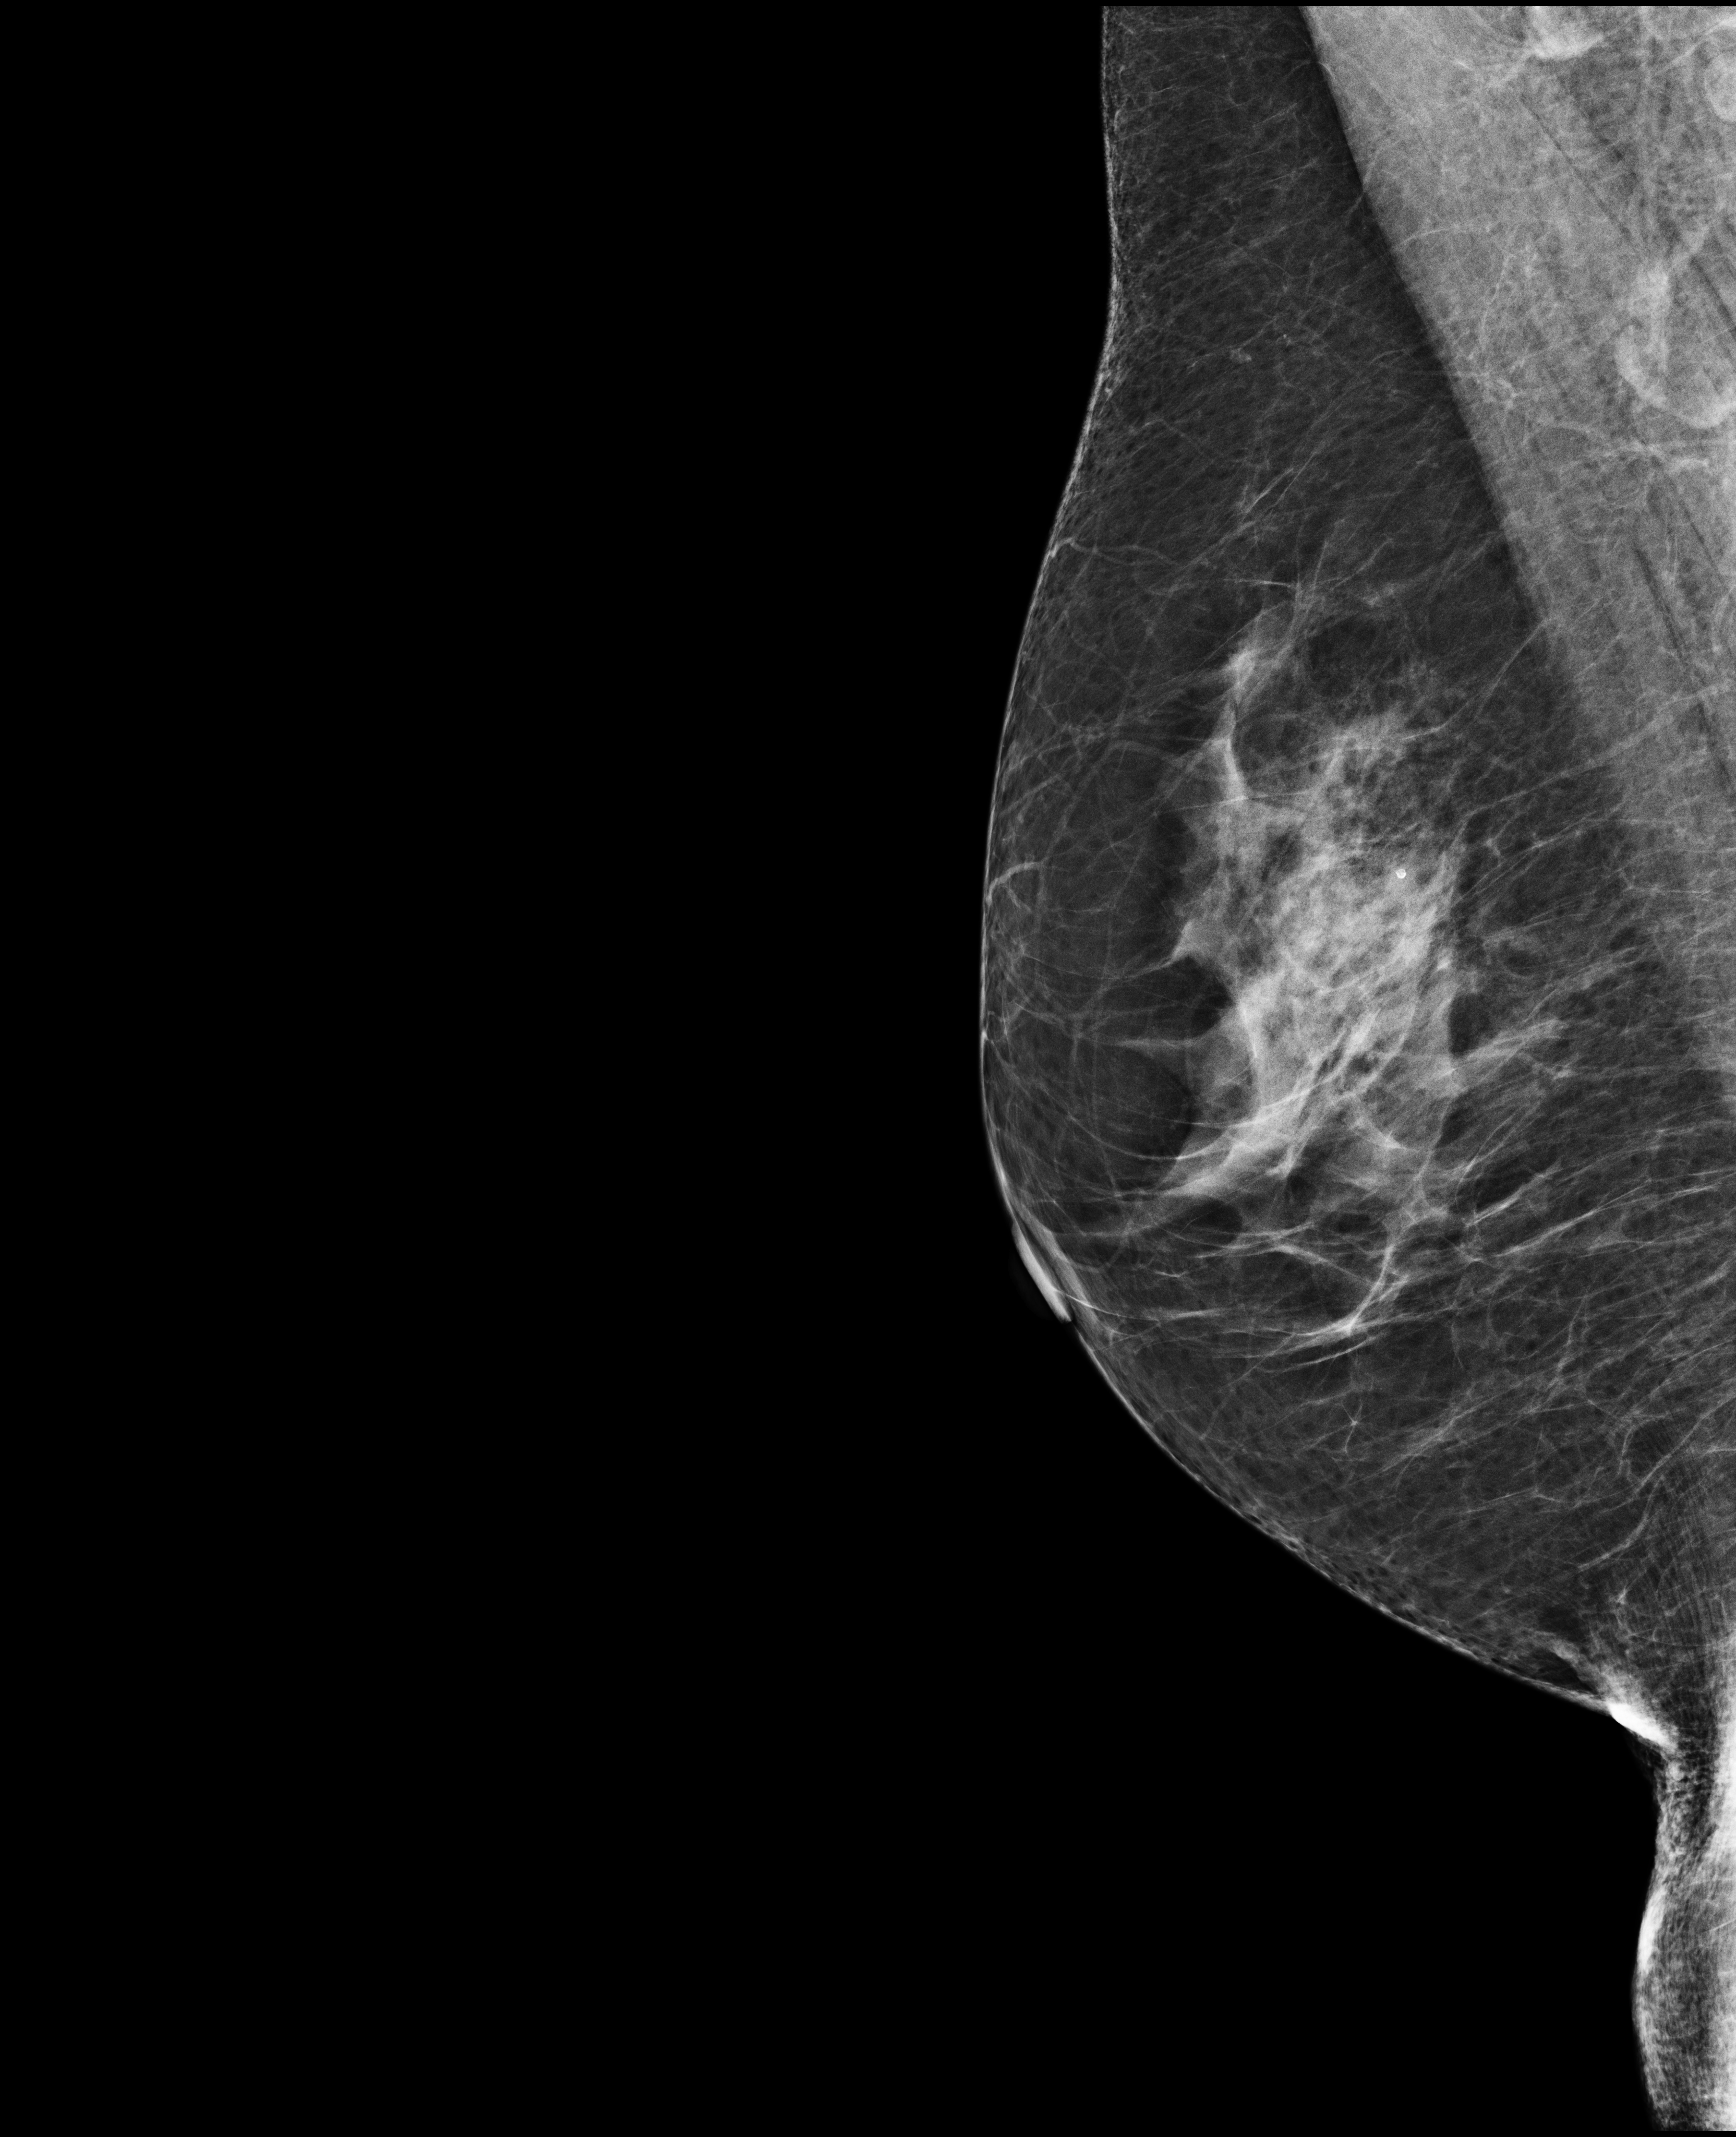
Screening examination, compressed breast thickness 66 mm. Patient: female, 64 years.
Image type: full-field digital mammogram. Breast: right. Projection: mediolateral oblique (MLO) view.